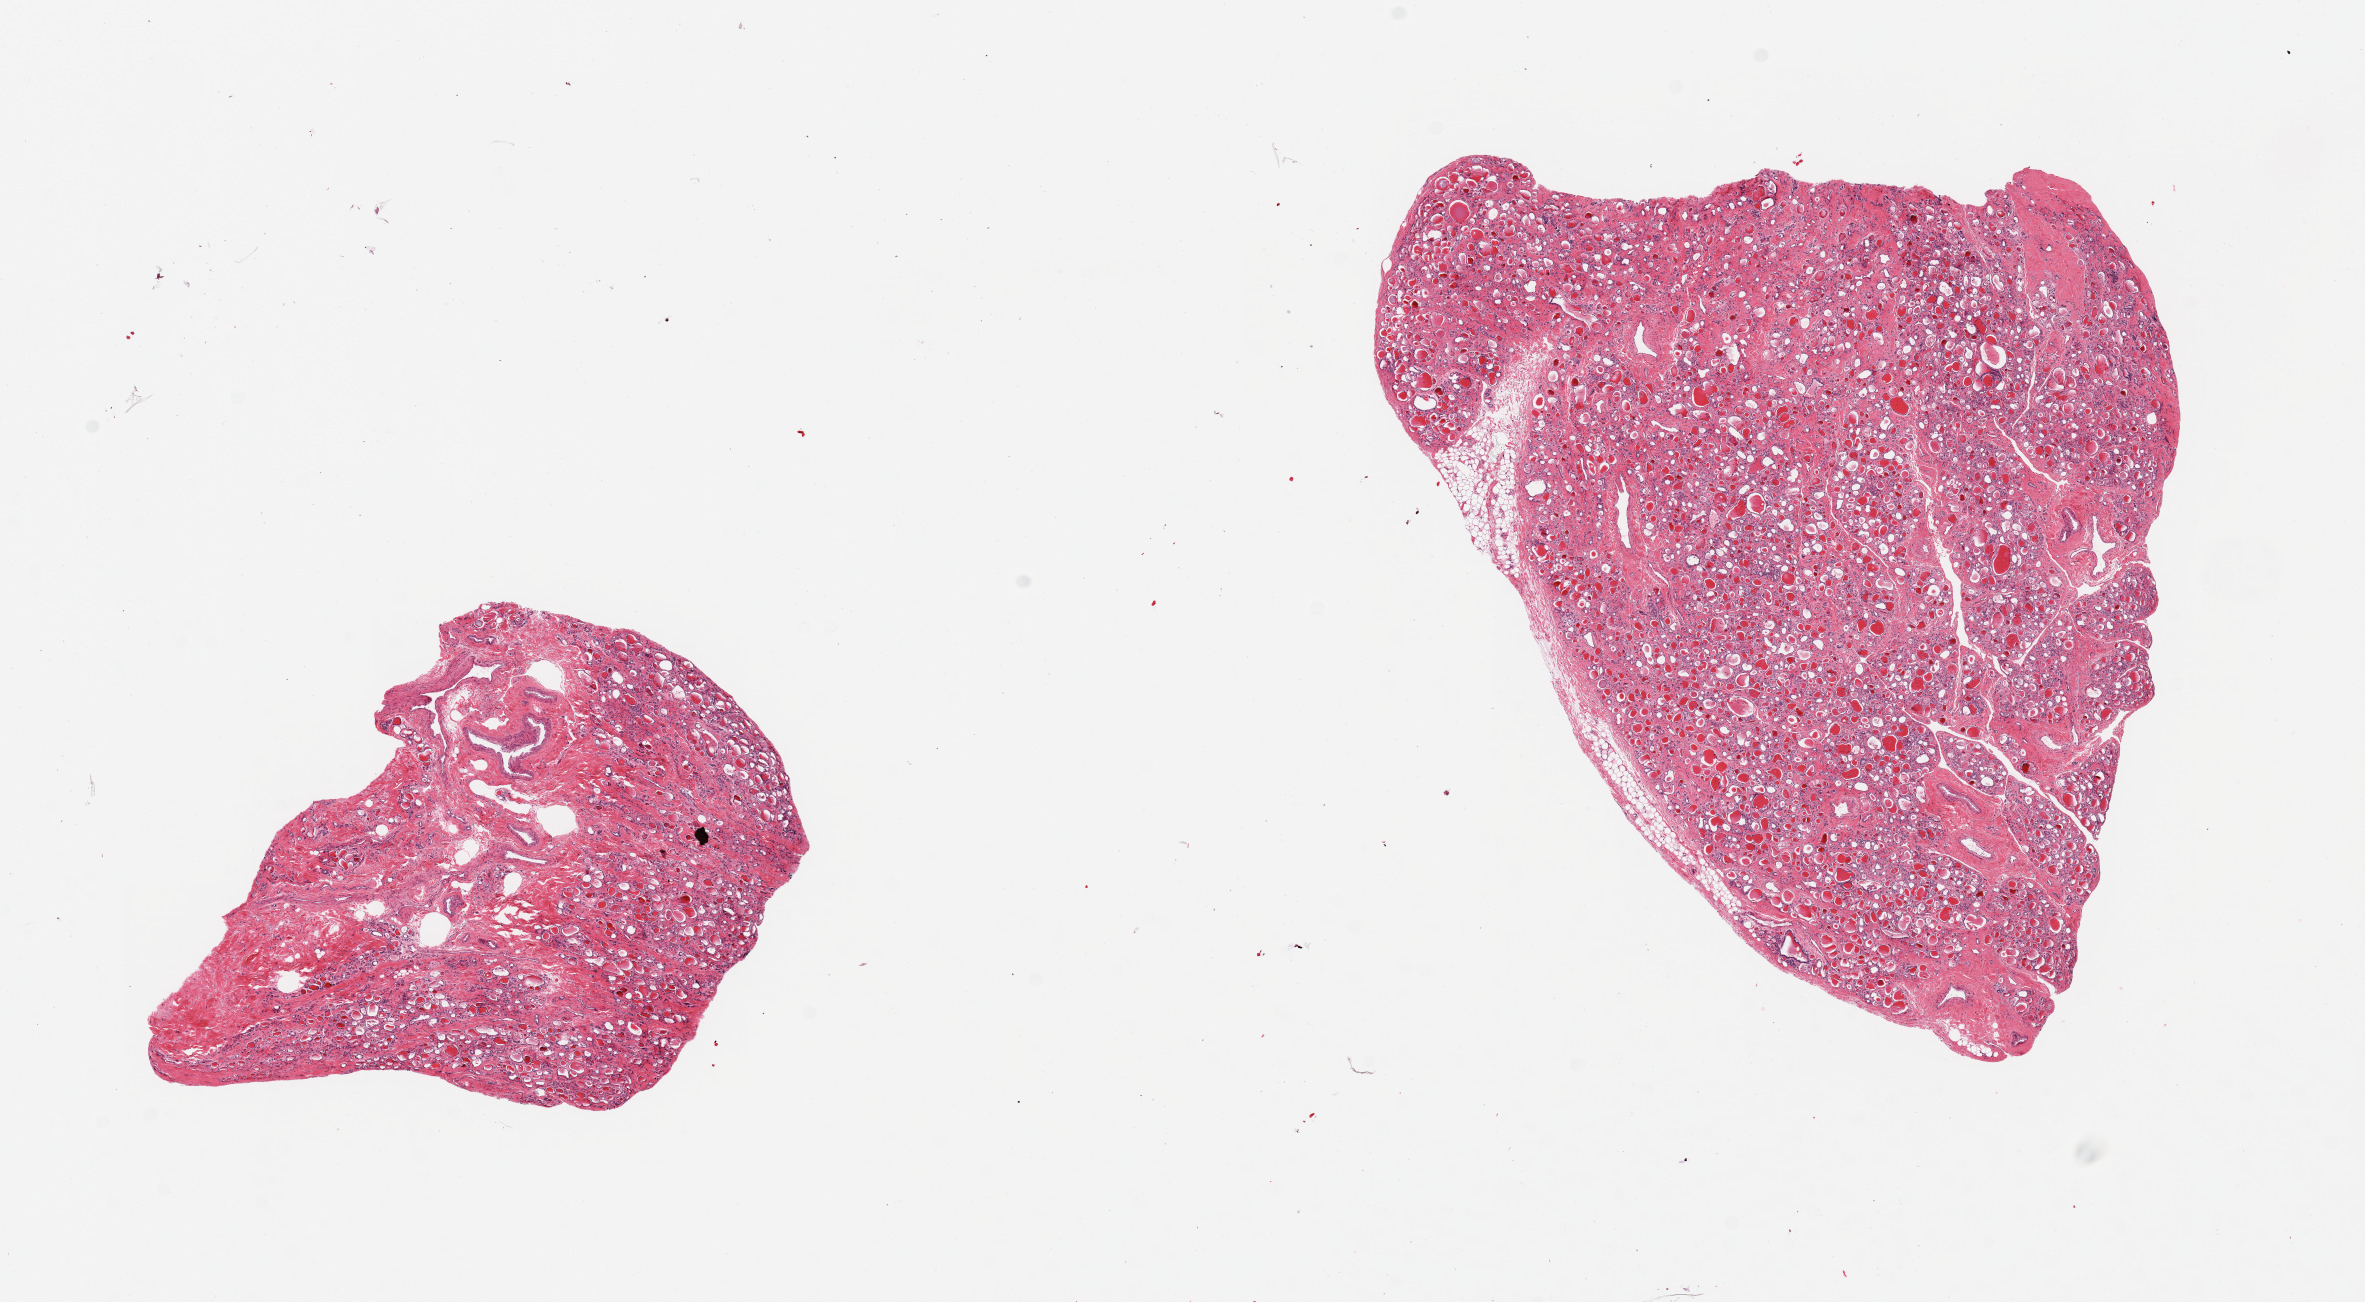
Hematoxylin and eosin (H&E) whole-slide image — a low-resolution overview of the entire scanned area, about 18.7 x 10.3 mm; PAXgene-fixed paraffin-embedded (PFPE) section; section of thyroid (target tissue); tissue donor sample. Donor sex: female.
Review note (as recorded): 2 pieces, fibrosis and atrophy, smaller piece is ~30% fibrous and vascular tissue.